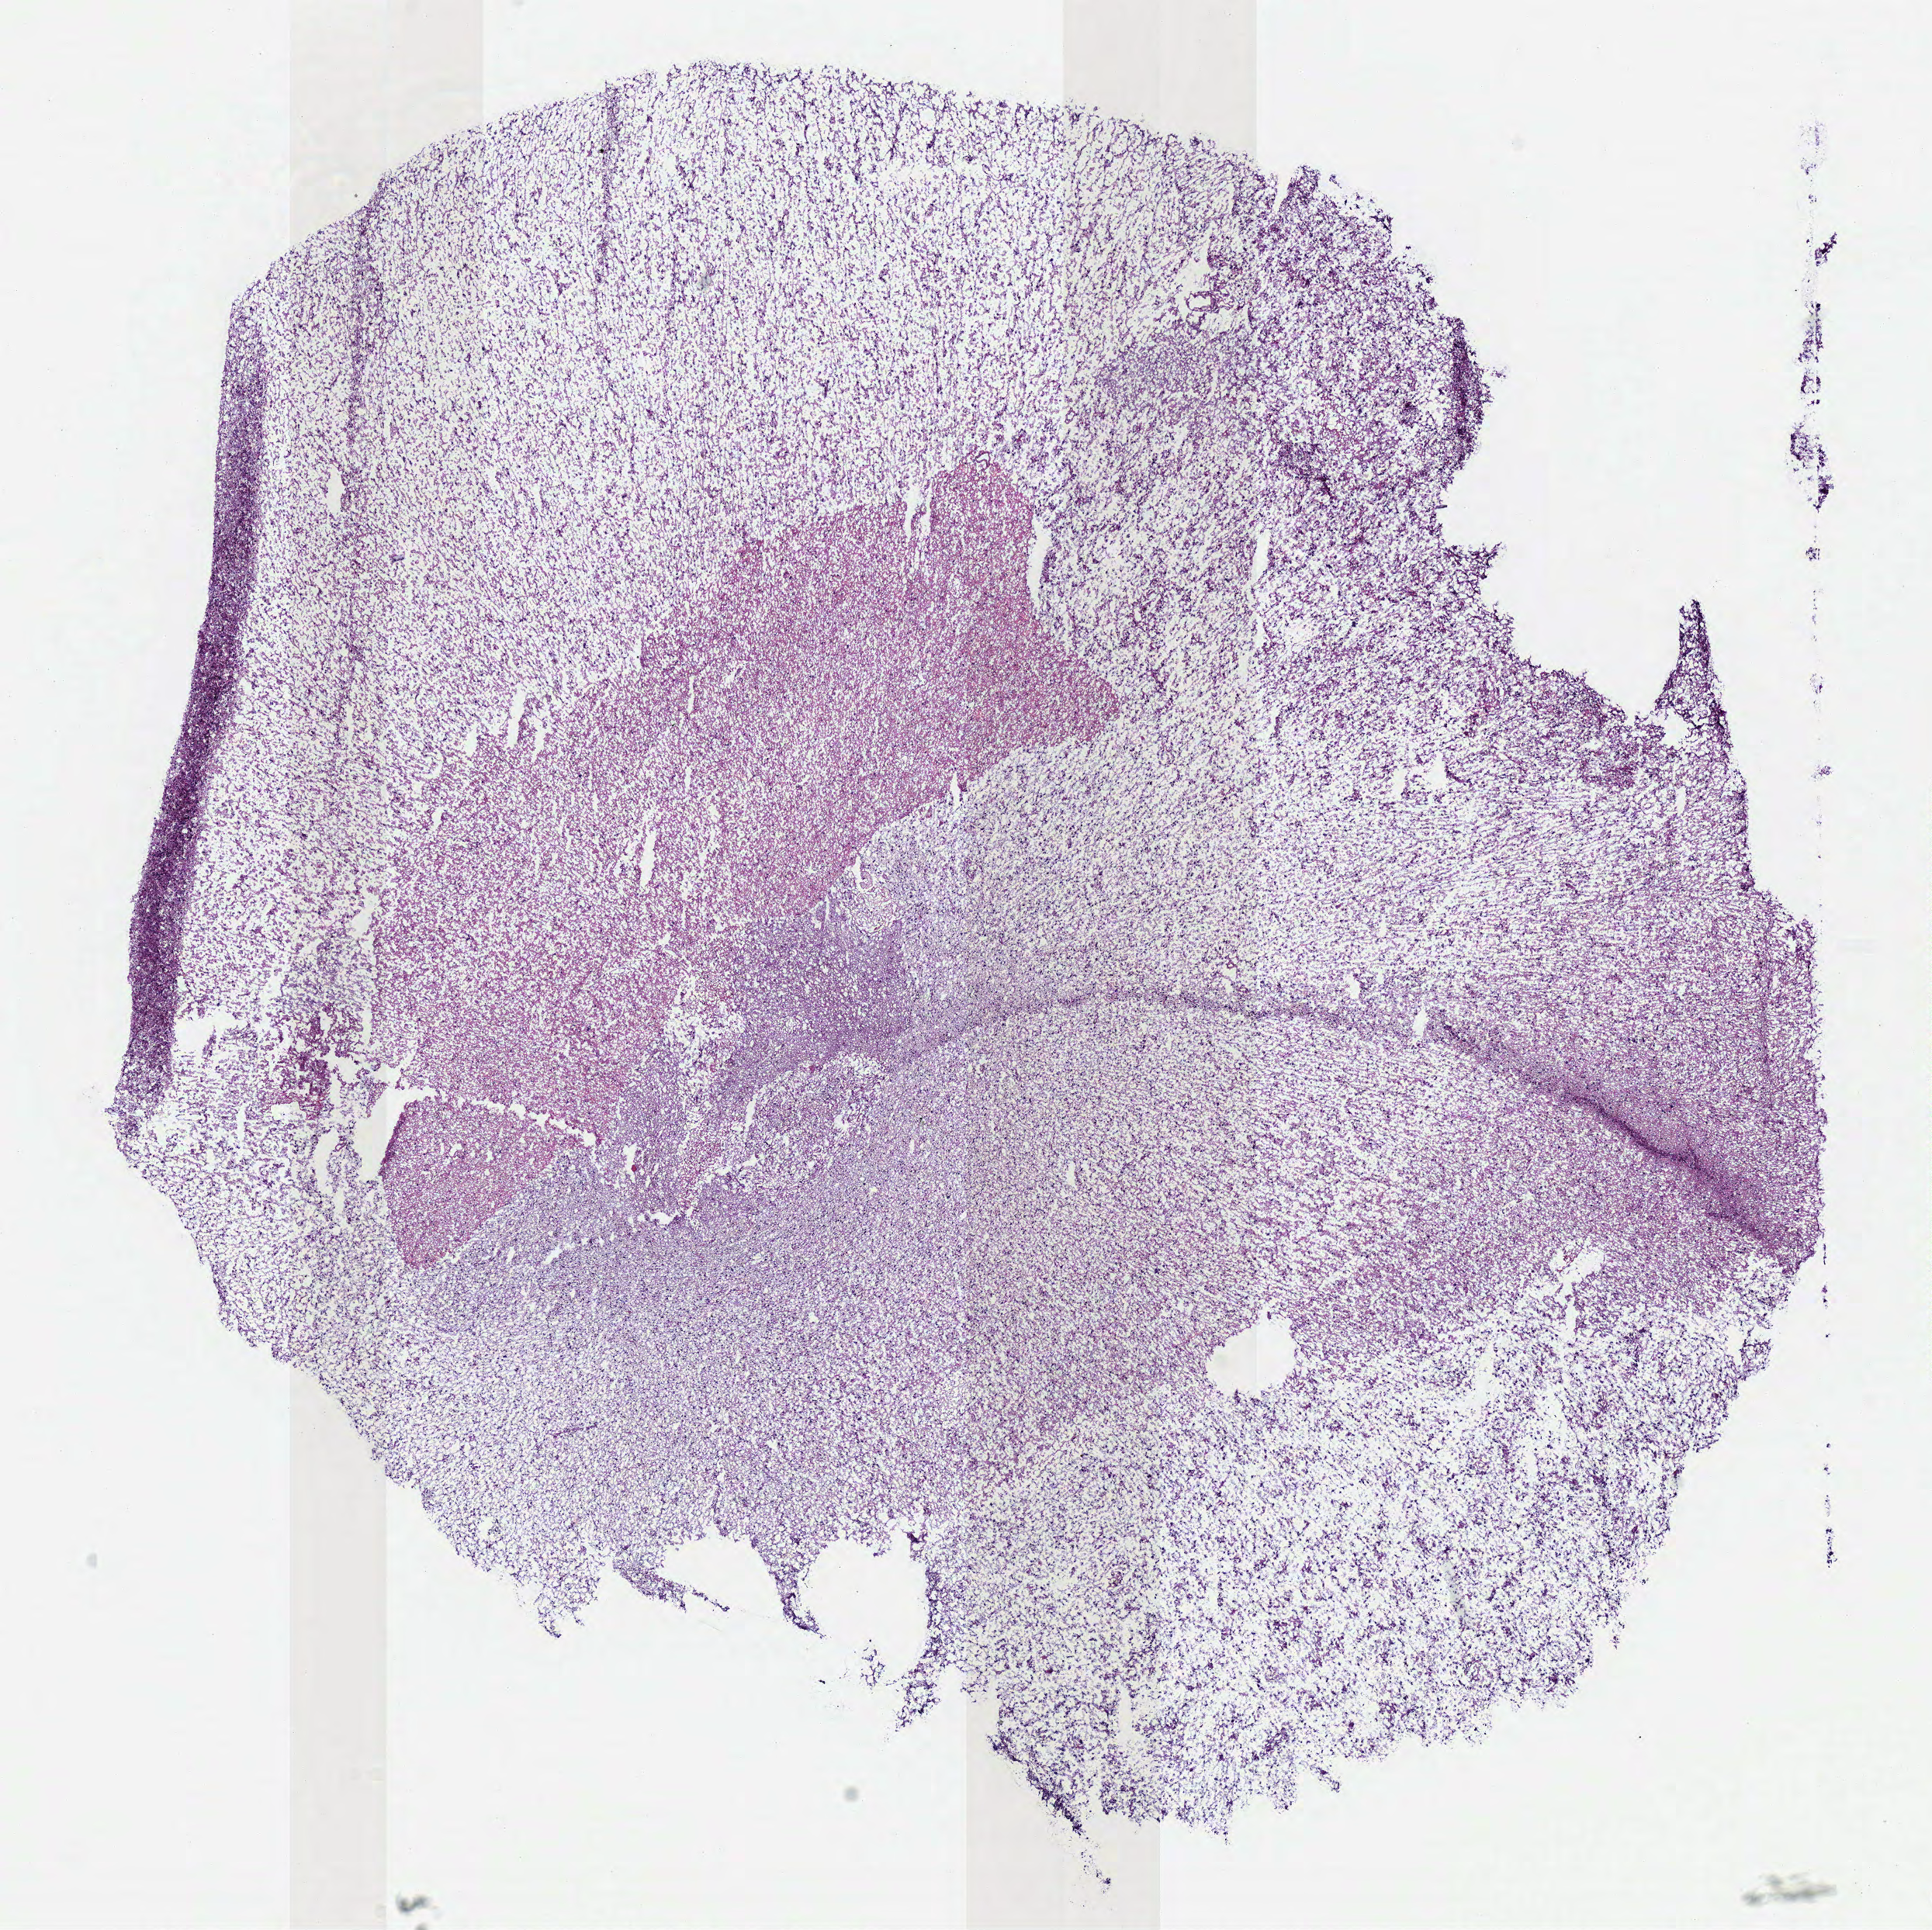
Hematoxylin and eosin (H&E) stained whole-slide image, low-resolution overview of the scanned area, about 9.8 x 9.8 mm (acquisition: 40x scan); frozen section from the bottom of the tissue portion; primary tumour sample from the brain. Female patient; age at initial diagnosis 58 years. Histologic grade: G3 (poorly differentiated). Composition of this section per pathologist review: tumour cells 100%, tumour nuclei 70%, normal cells 0%, stromal cells 0%, necrosis 0%.
Histologic diagnosis: Astrocytoma, anaplastic (cerebrum).